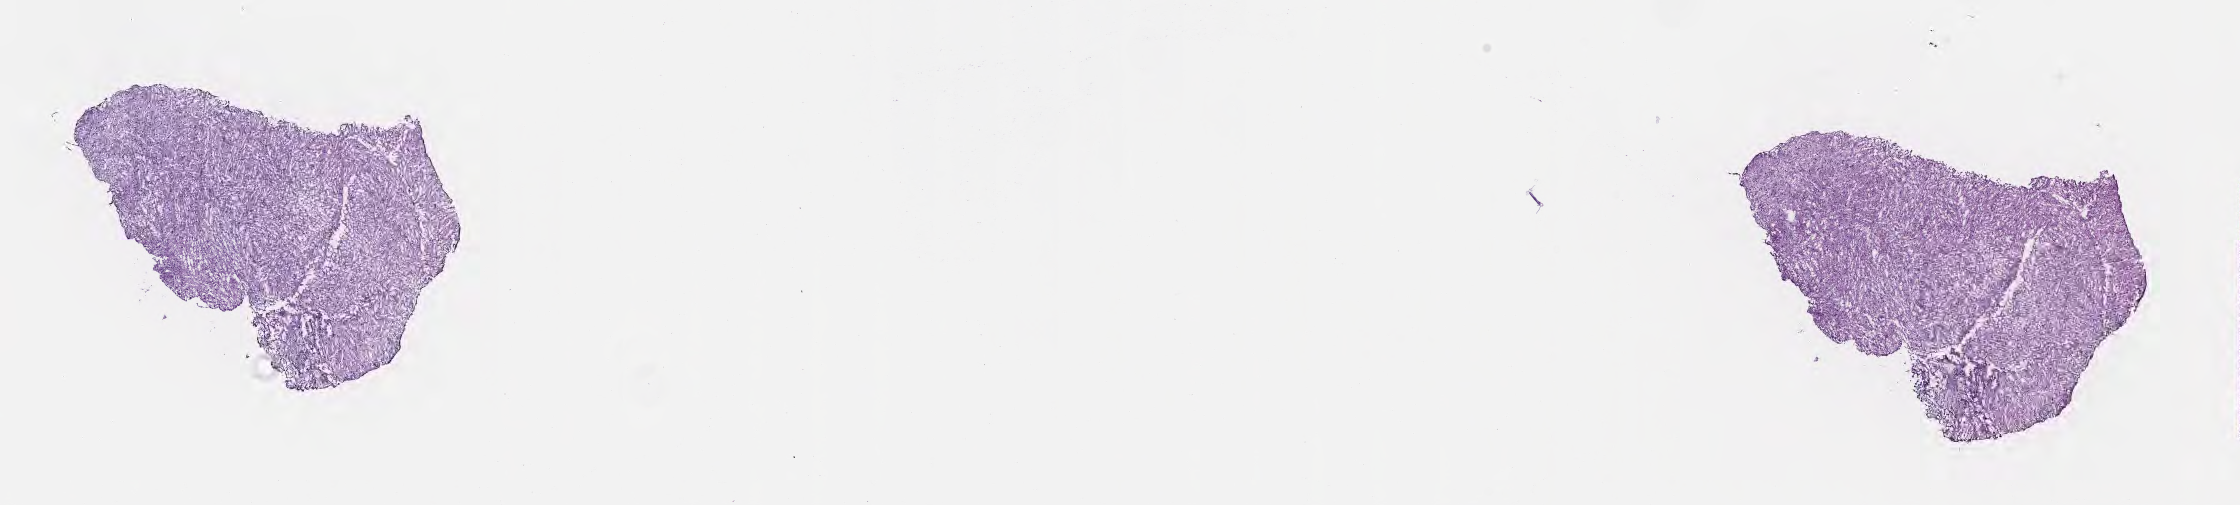
Haematoxylin and eosin whole-slide image — shown as a low-resolution overview of the whole scanned area (about 18.1 x 4.1 mm), frozen section, specimen: primary tumor, anatomic site: brain. Patient: female, age at initial diagnosis 63 years. Slide review estimates, as recorded: tumor cells 85%, tumor nuclei 93%.
Histologic diagnosis: Glioblastoma, NOS.